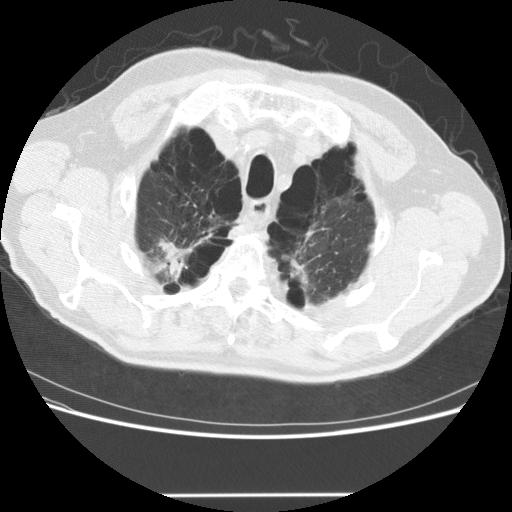
Low-dose screening chest CT, axial slice. Third screening round (two years after baseline). Lung window (W 1500 / L -600 HU). 2.5 mm slice thickness. Male, age 68 years at enrolment.
Lesion marked by an expert reader, box from (x=130, y=215) to (x=215, y=293) px. The screening reader recorded 2 non-calcified nodules or masses ≥4 mm on this exam (lingula, left lower lobe); which of them this box marks is not recorded. Later outcome: lung cancer diagnosed 301 days after this screen — large cell carcinoma, NOS, right upper lobe, poorly differentiated (G3), stage IV (AJCC 6th edition).